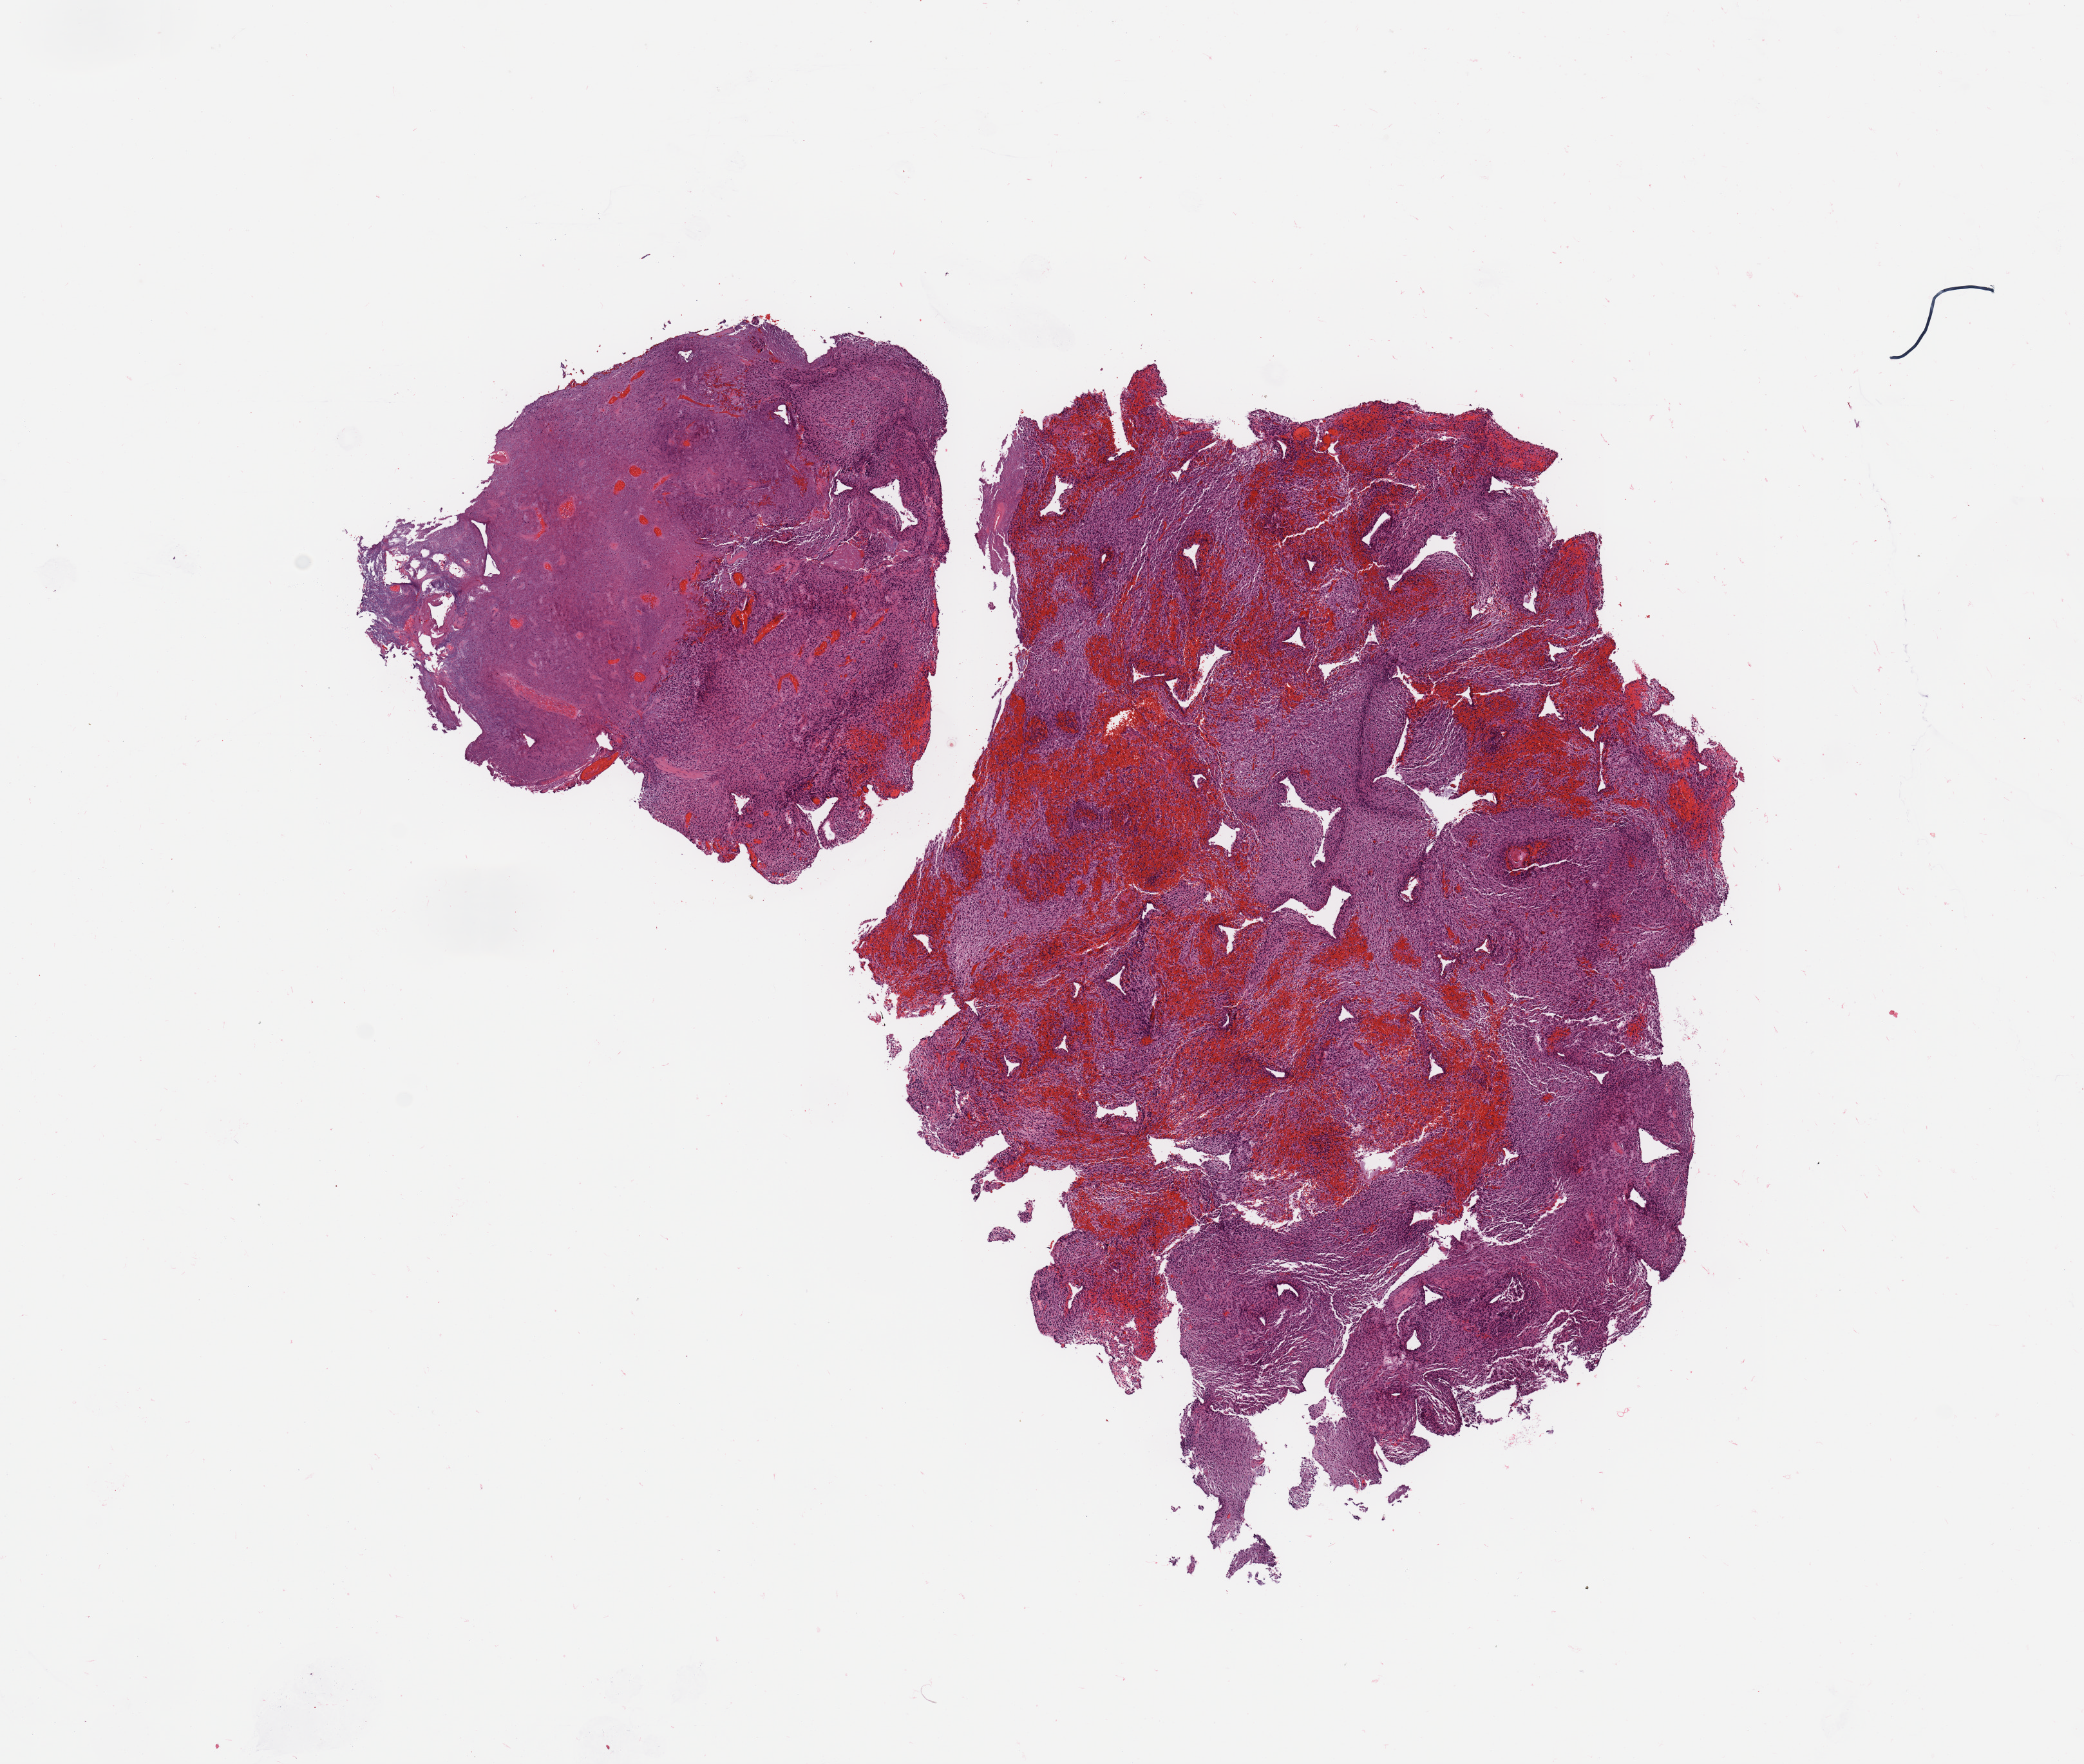
H&E whole-slide image, shown as a low-resolution overview of the whole scanned area (about 12.8 x 10.8 mm, acquisition: 20x scan), tumour tissue sample, sampled site: frontal lobe. 74-year-old male patient. Slide review estimates, as recorded: tumour nuclei 90%, necrosis 20%.
Diagnosis: Glioblastoma. Primary tumour site (as recorded): frontal lobe.